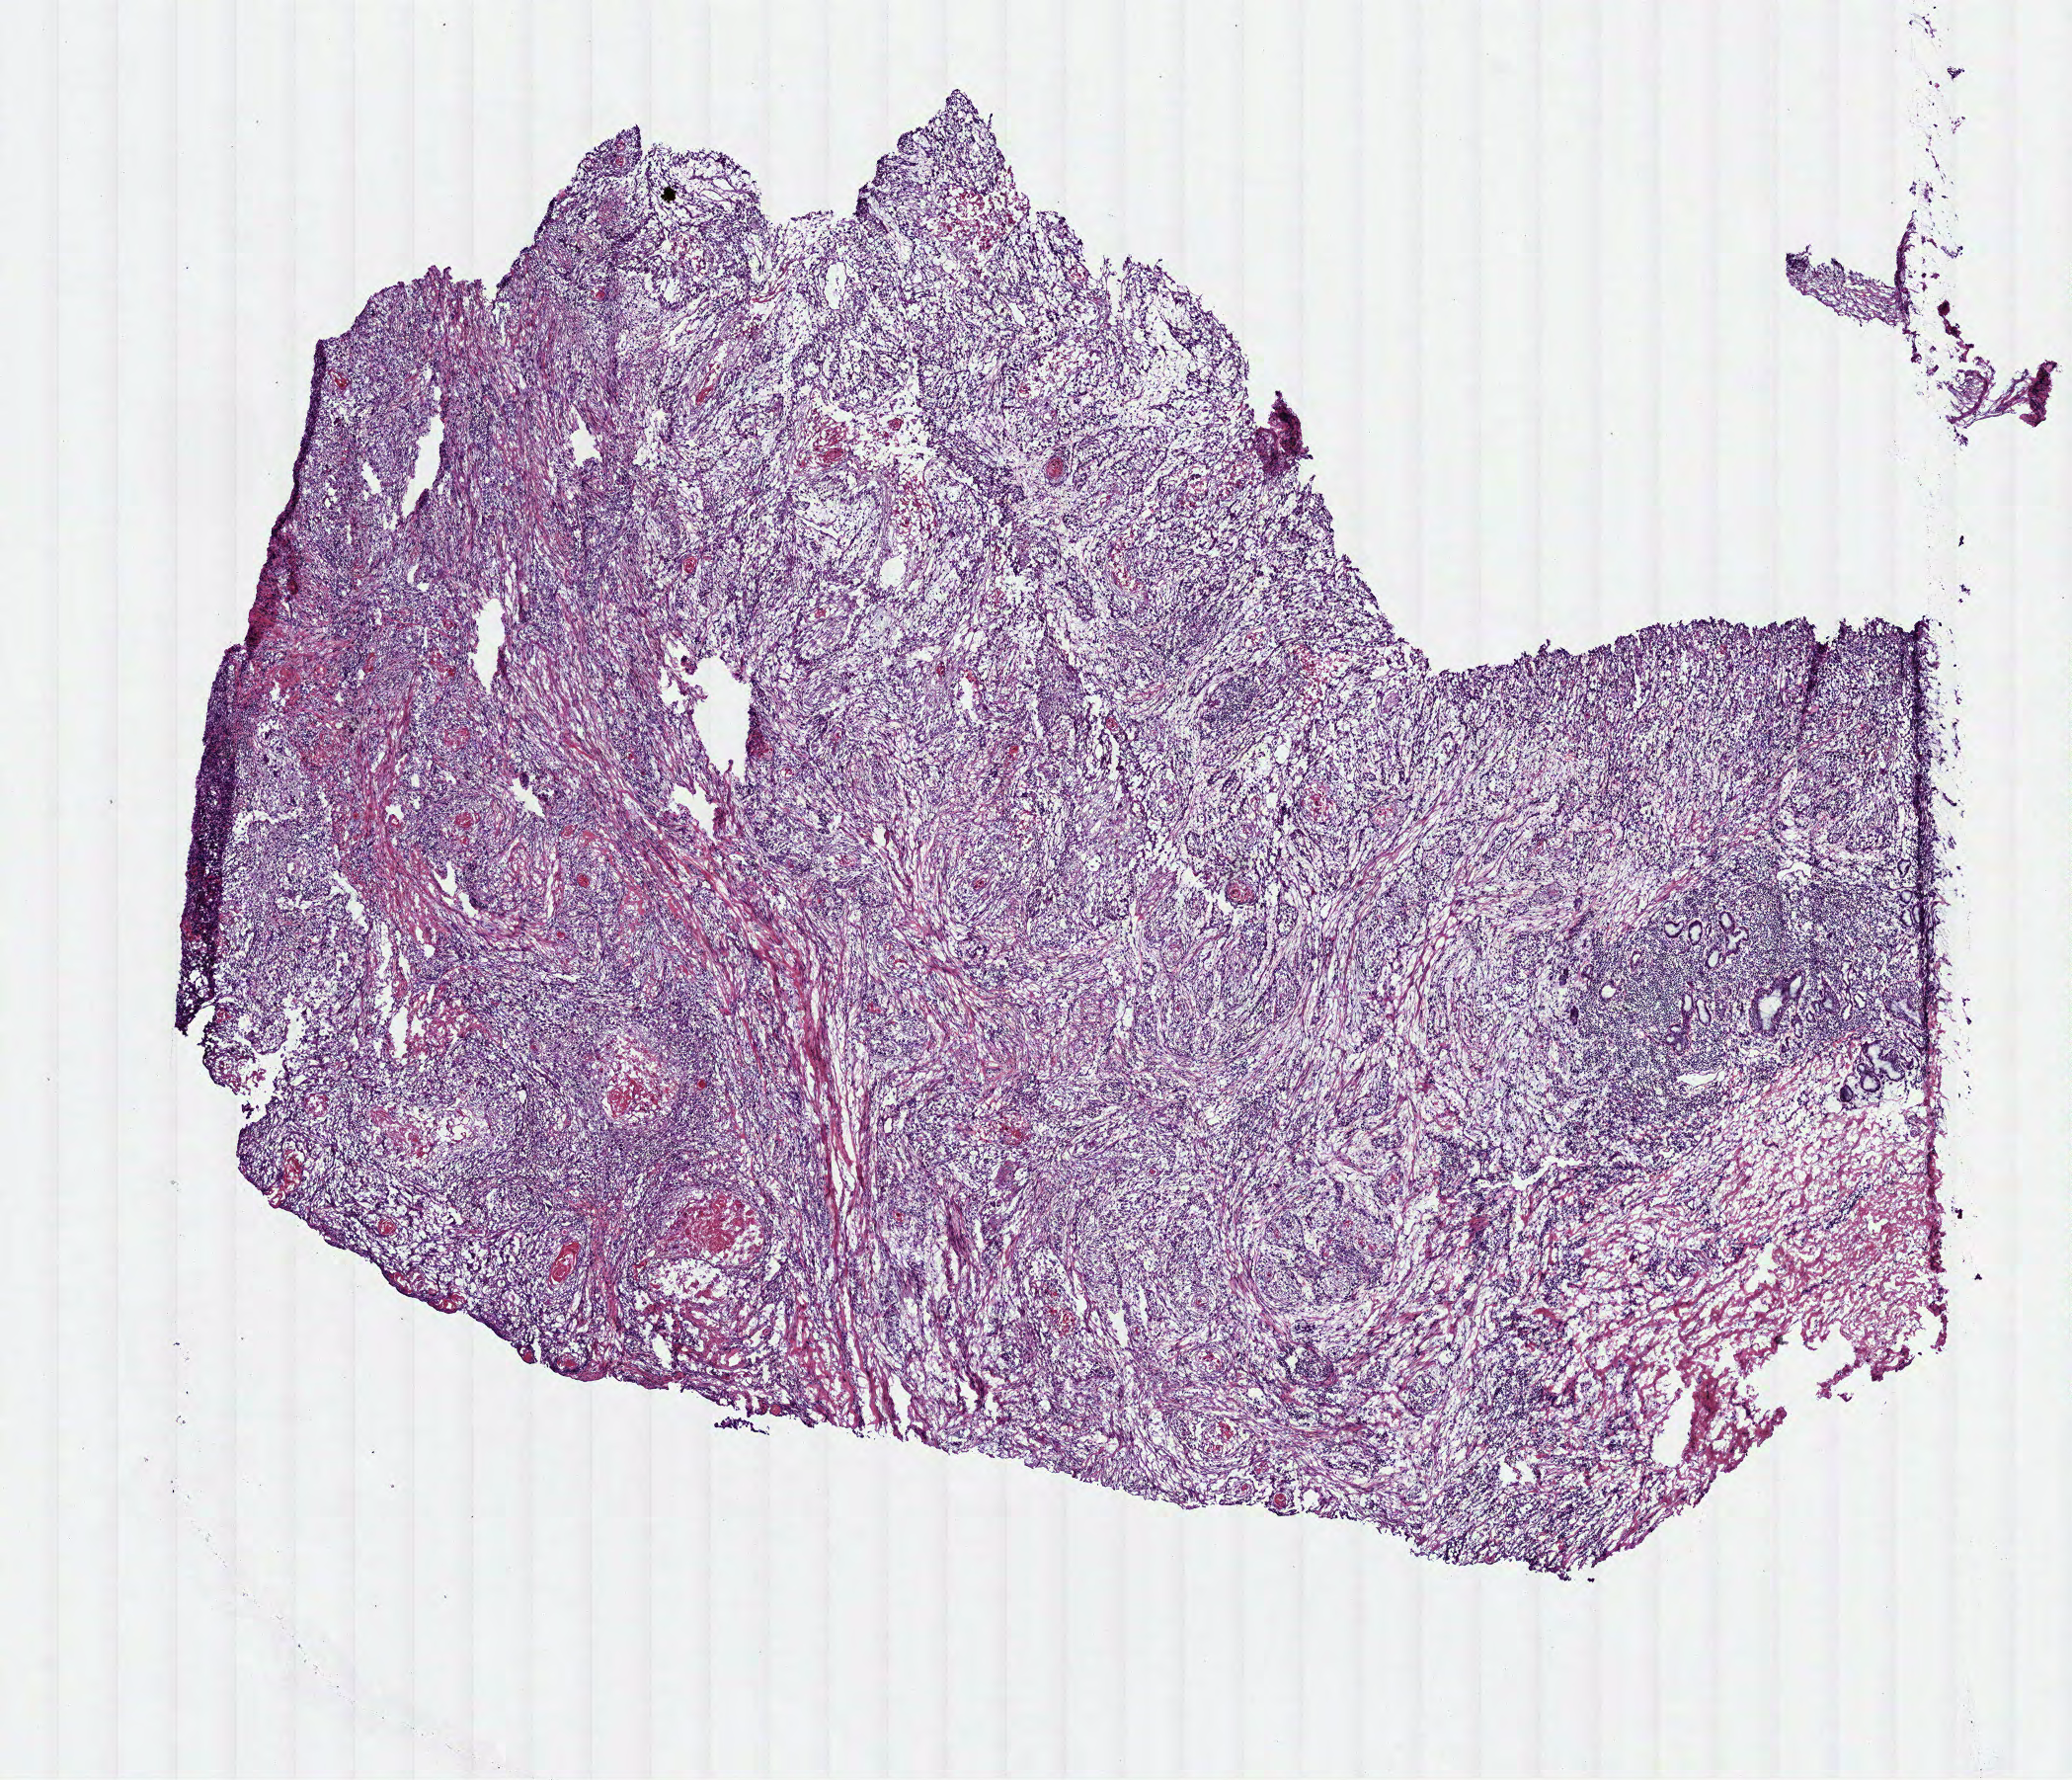
Hematoxylin and eosin (H&E) stained whole-slide image — low-resolution overview of the scanned area, about 8.5 x 7.3 mm; frozen section; sample: primary tumour, head and neck. Patient: male, age at initial diagnosis 49 years. Histologic grade: G3 (poorly differentiated). Pathologist review of this section (percent, as recorded): tumour cells 80%, tumour nuclei 65%, normal cells 0%, stromal cells 20%, necrosis 0%.
AJCC pathologic stage: IVA (7th edition). Pathologic diagnosis: Squamous cell carcinoma, NOS (larynx, NOS).